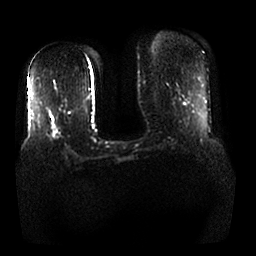
Breast MRI, one axial slice. Slice 11 of 25 in the series (ordered by position). Diffusion-weighted series; image 2 of 4 stored at this slice position (different b-values; order by instance number). 1.5 T. 4 mm slice thickness. 256 × 256 image matrix. Female patient.
Outlined on this slice (manually delineated by an expert):
- tumour on diffusion-weighted imaging: bounding box <51,121,56,133> (left, top, right, bottom; pixels)